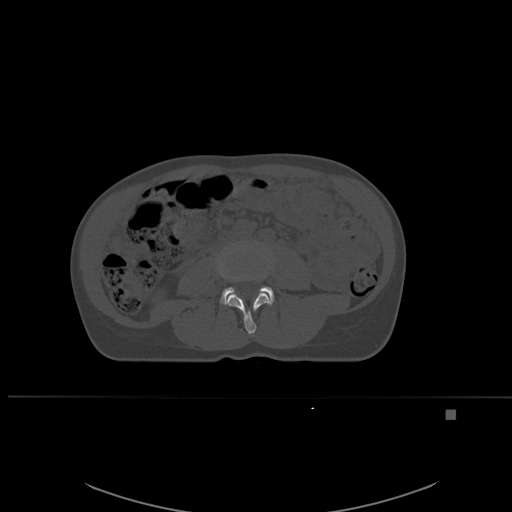
CT including the spine, one axial slice; position 204 of 537 along the scan axis; bone window (W 1800 / L 400 HU); 1.5 mm slice thickness; 512 × 512 image matrix. Patient: female, 45 years. Case-level facts recorded for this patient, not image findings: primary cancer: lung.
Annotated regions visible in this slice (semi-automatically segmented with operator editing):
- L3 vertebra: bounding box (x1, y1, x2, y2) in pixels: (218, 247, 270, 334)
- L4 vertebra: (220, 286, 274, 305)